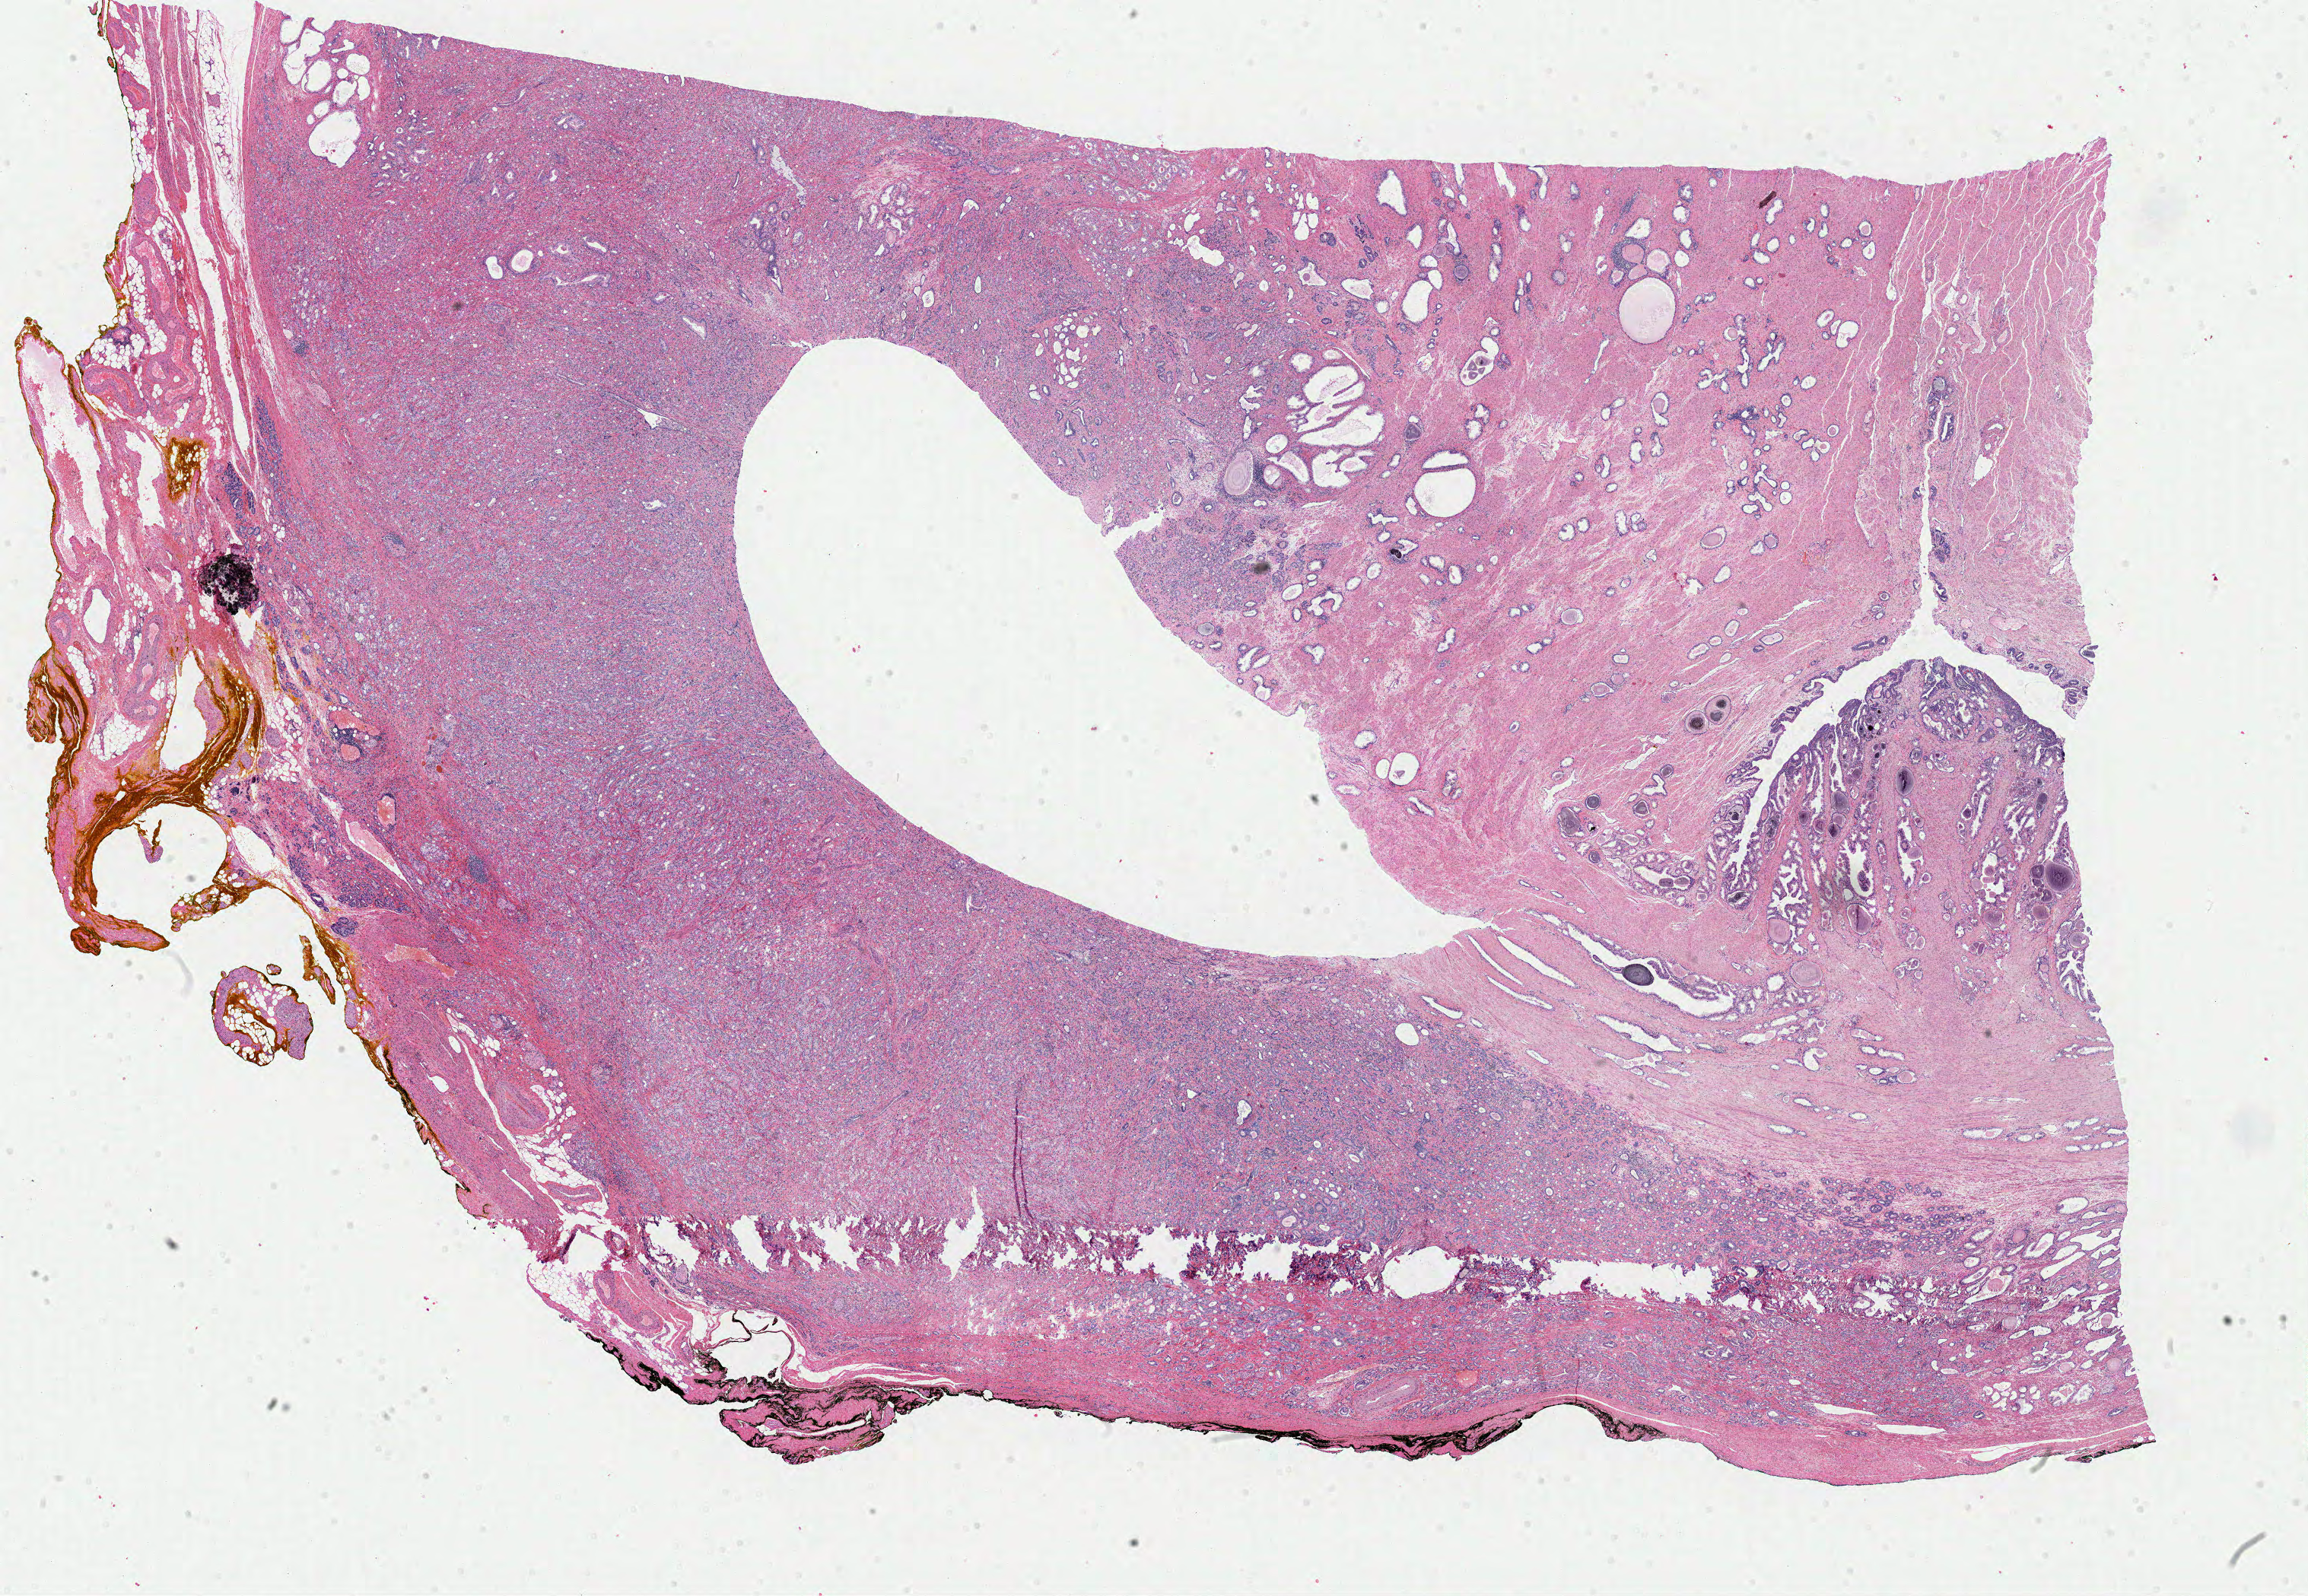
Whole-slide histology image, H&E-stained — shown as a low-resolution overview of the whole scanned area (about 24.0 x 16.6 mm). Formalin-fixed paraffin-embedded (FFPE) diagnostic section. Primary tumour sample from the prostate. Male patient; age at initial diagnosis 69 years. Gleason score: 9 (4+5).
• diagnosis: Adenocarcinoma, NOS (prostate gland)
• lymph nodes positive (case pathology): 0 of 5 examined